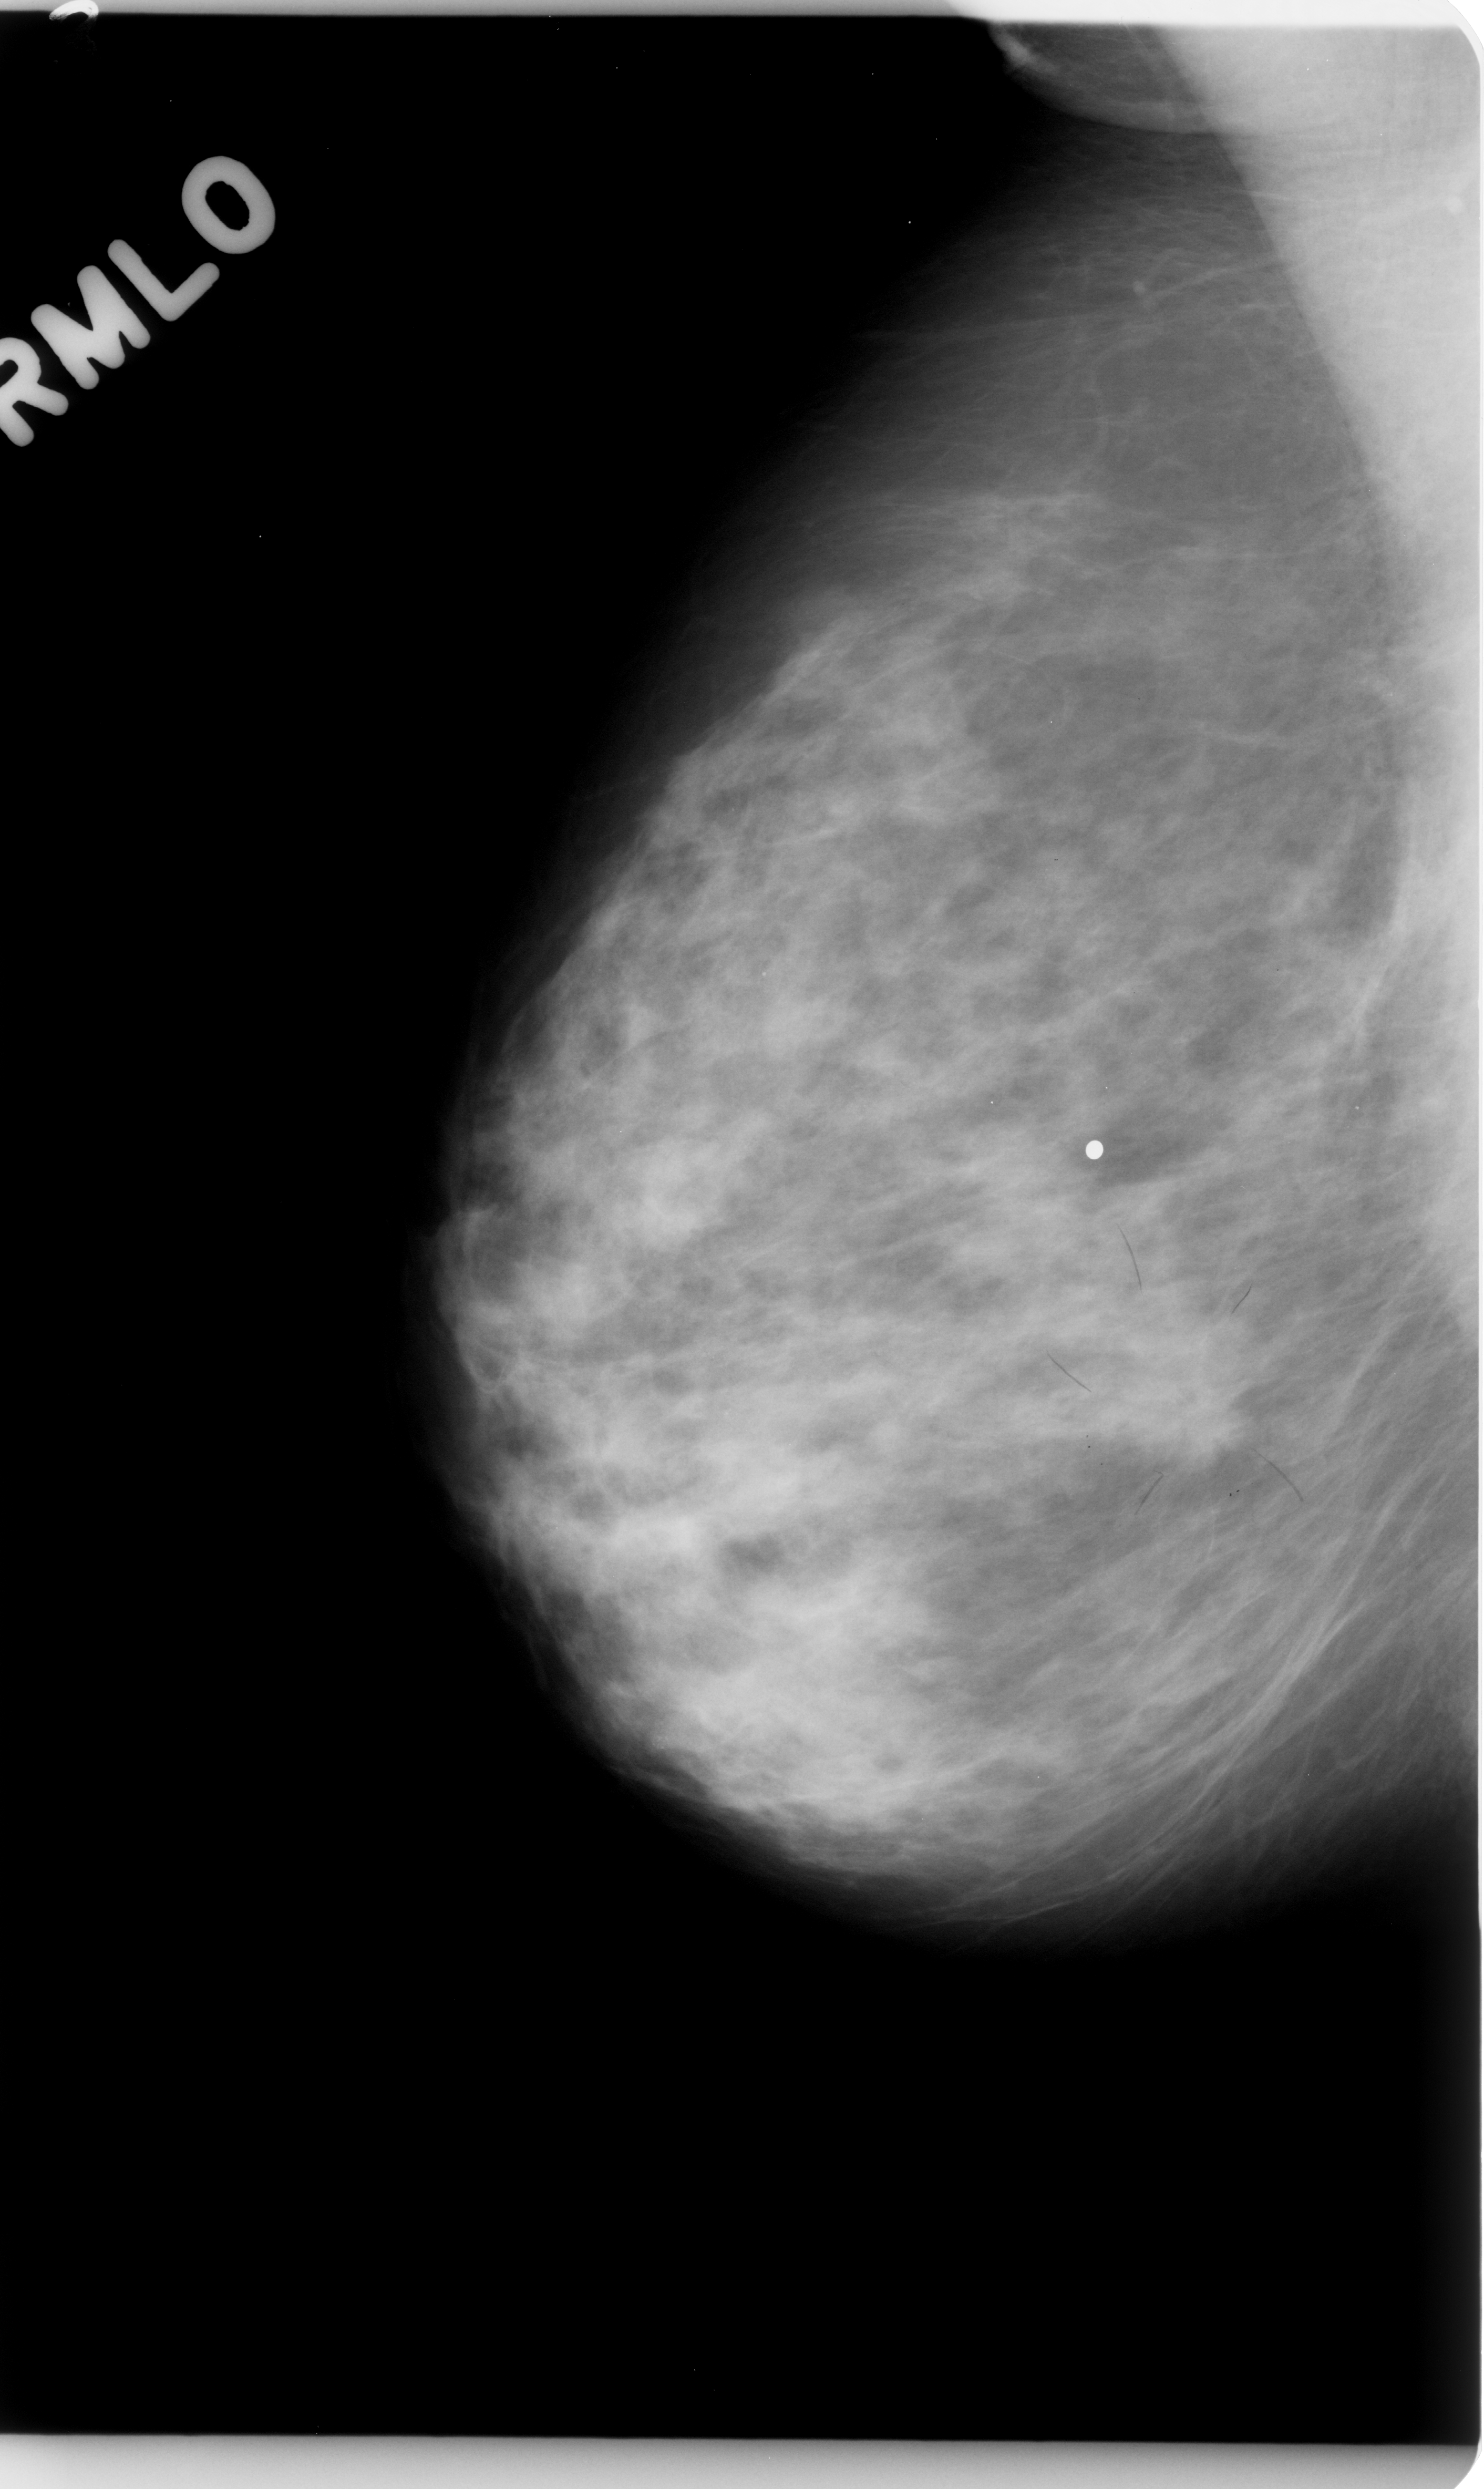
Mammogram (digitized film); right breast; MLO view.
- Marked abnormality: mass, shape irregular, margins spiculated; BI-RADS assessment category 4; subtlety rating 3 on a 1 (subtle) to 5 (obvious) scale; pathology result (as recorded, not read from the image): malignant.